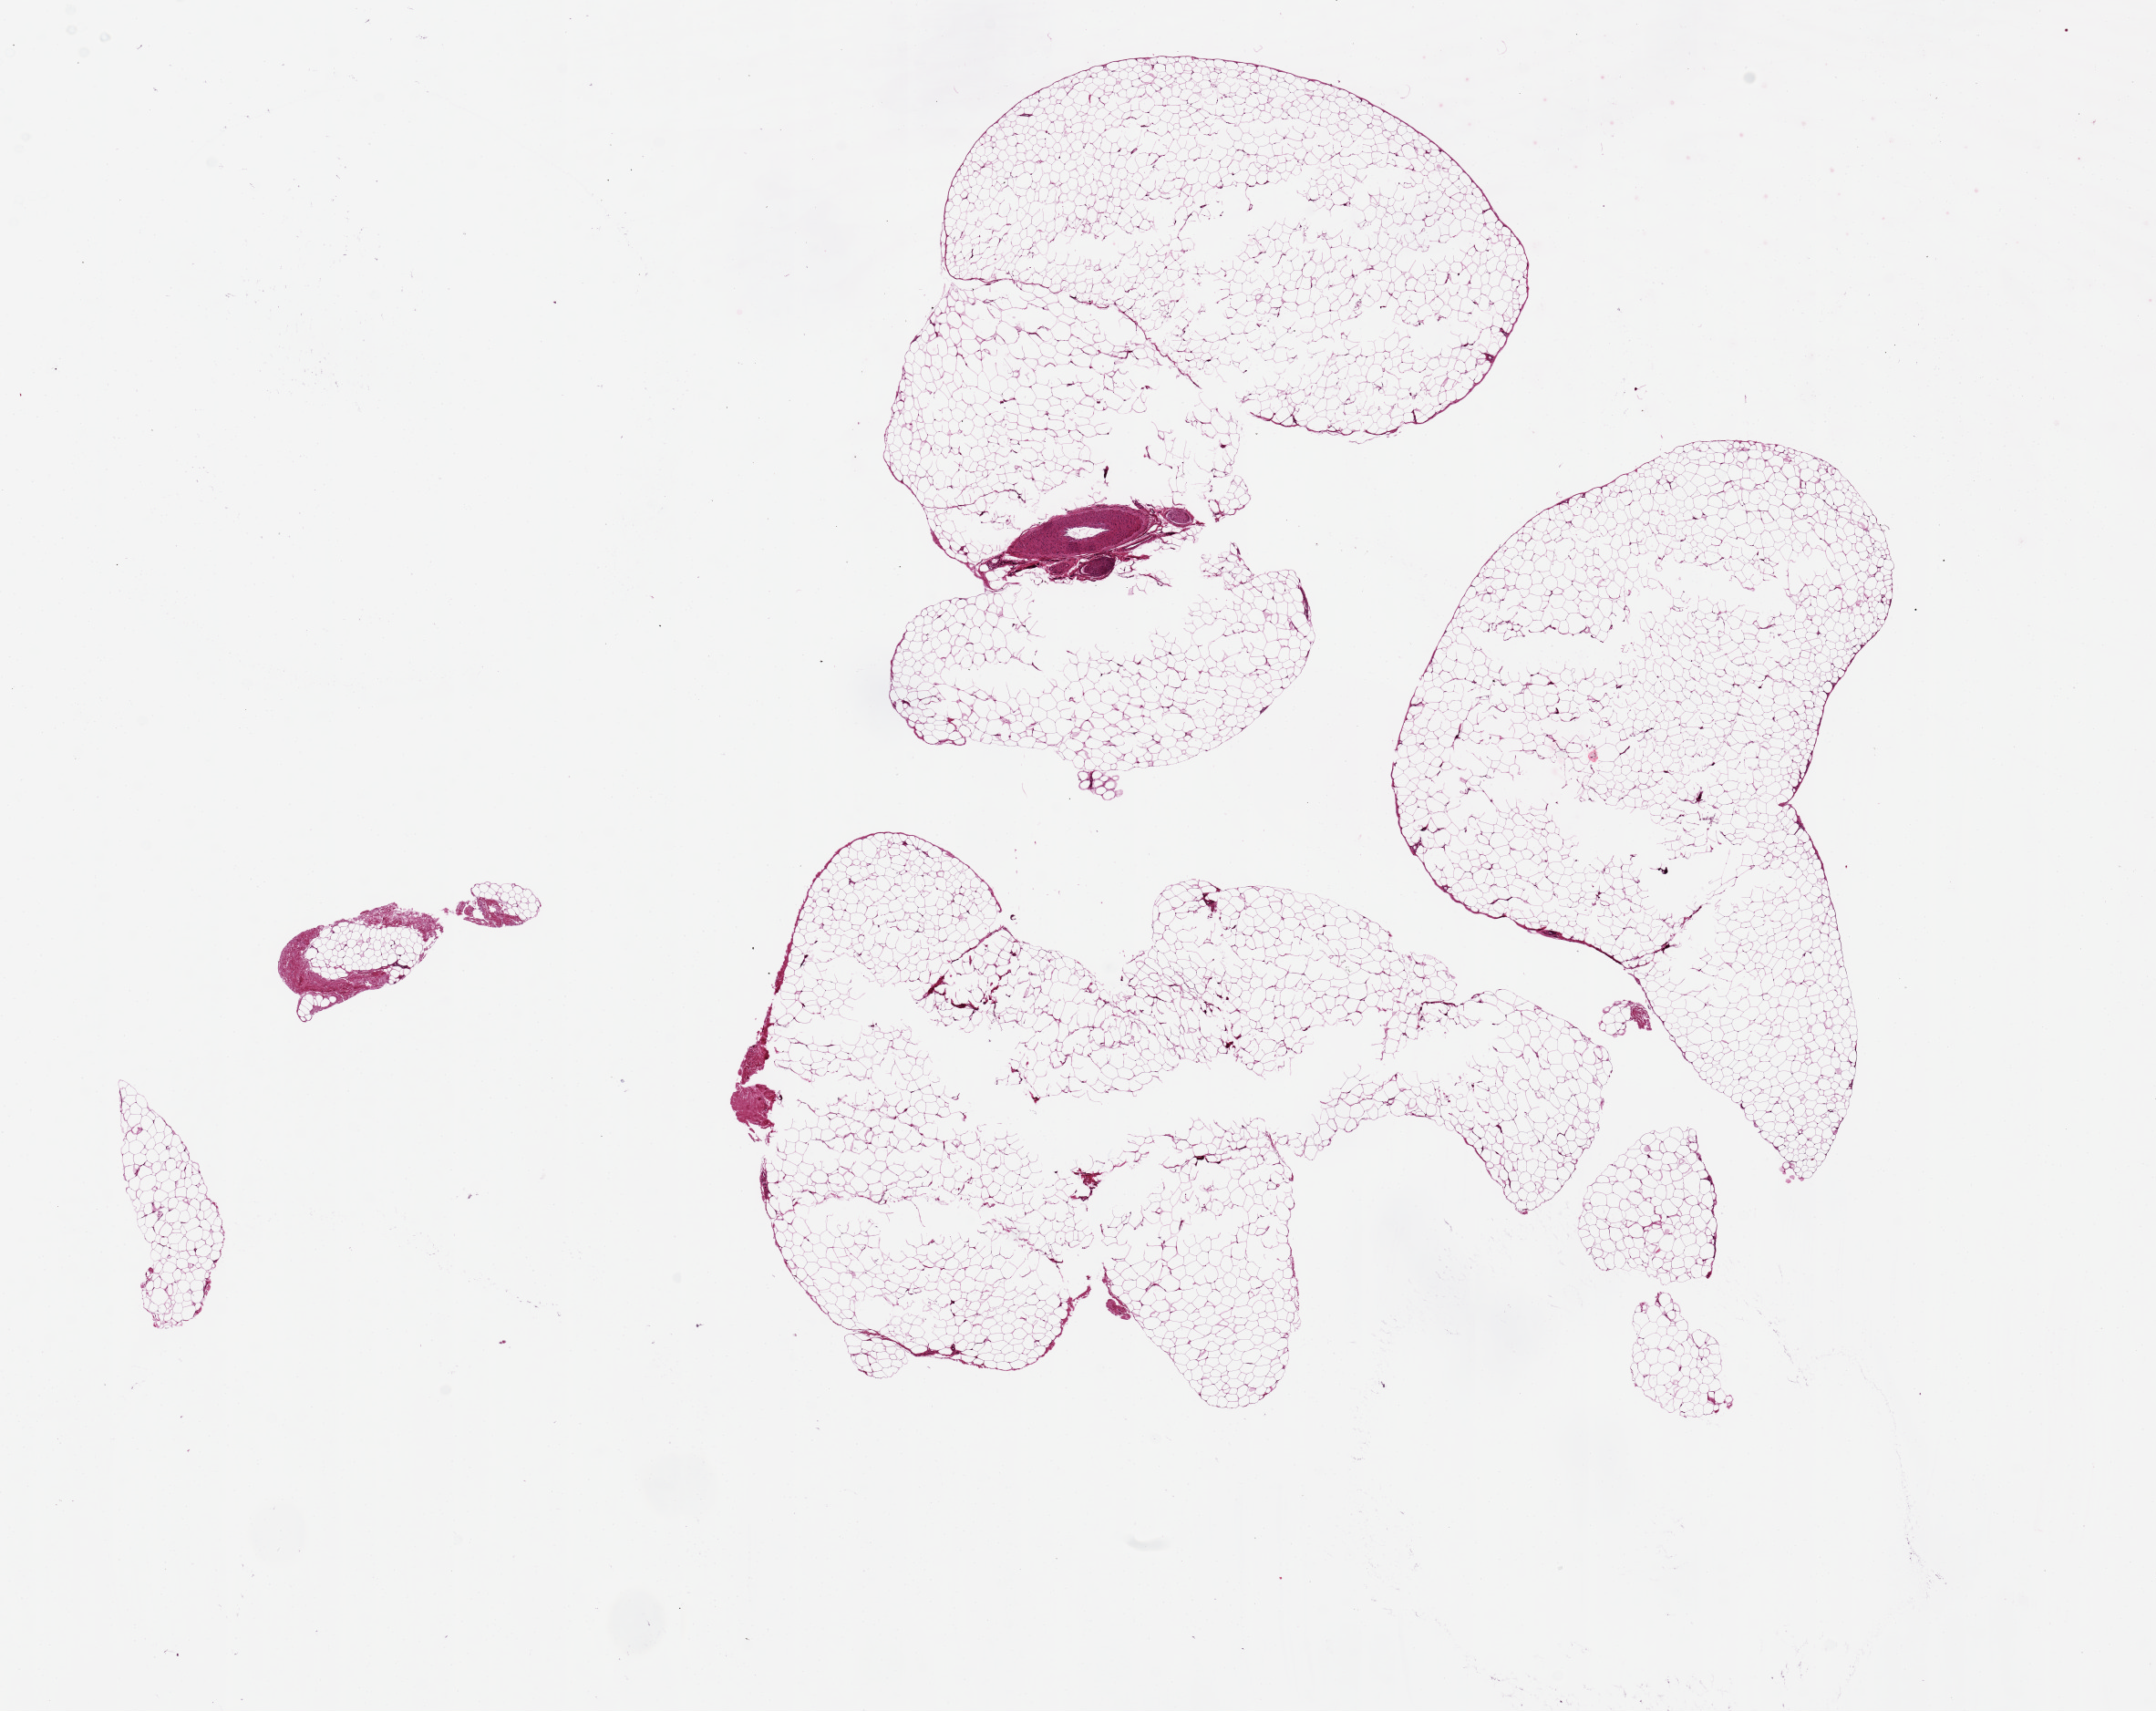
Digitized hematoxylin and eosin (H&E)-stained section, brightfield — low-resolution overview of the scanned area, about 18.7 x 14.8 mm. PAXgene-fixed paraffin-embedded (PFPE) section. Sampled site (target tissue): adipose tissue. Tissue donor sample. Donor: male.
Reviewer comment on this tissue sample: OK for analysis.